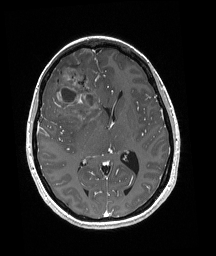
Brain MRI from a brain-tumour surgery series, one axial slice; slice 95 of 192 in the series (ordered by position); T1-weighted post-contrast; 1 mm slice thickness; 216 × 256 image matrix. Case-level facts recorded for this patient, not image findings: histopathology: Oligodendroglioma; WHO grade: 3; IDH mutation: yes; tumour location: Right Frontal.
Annotated regions visible in this slice (manually delineated by an expert):
- tumour: box from (x=50, y=59) to (x=98, y=118) px